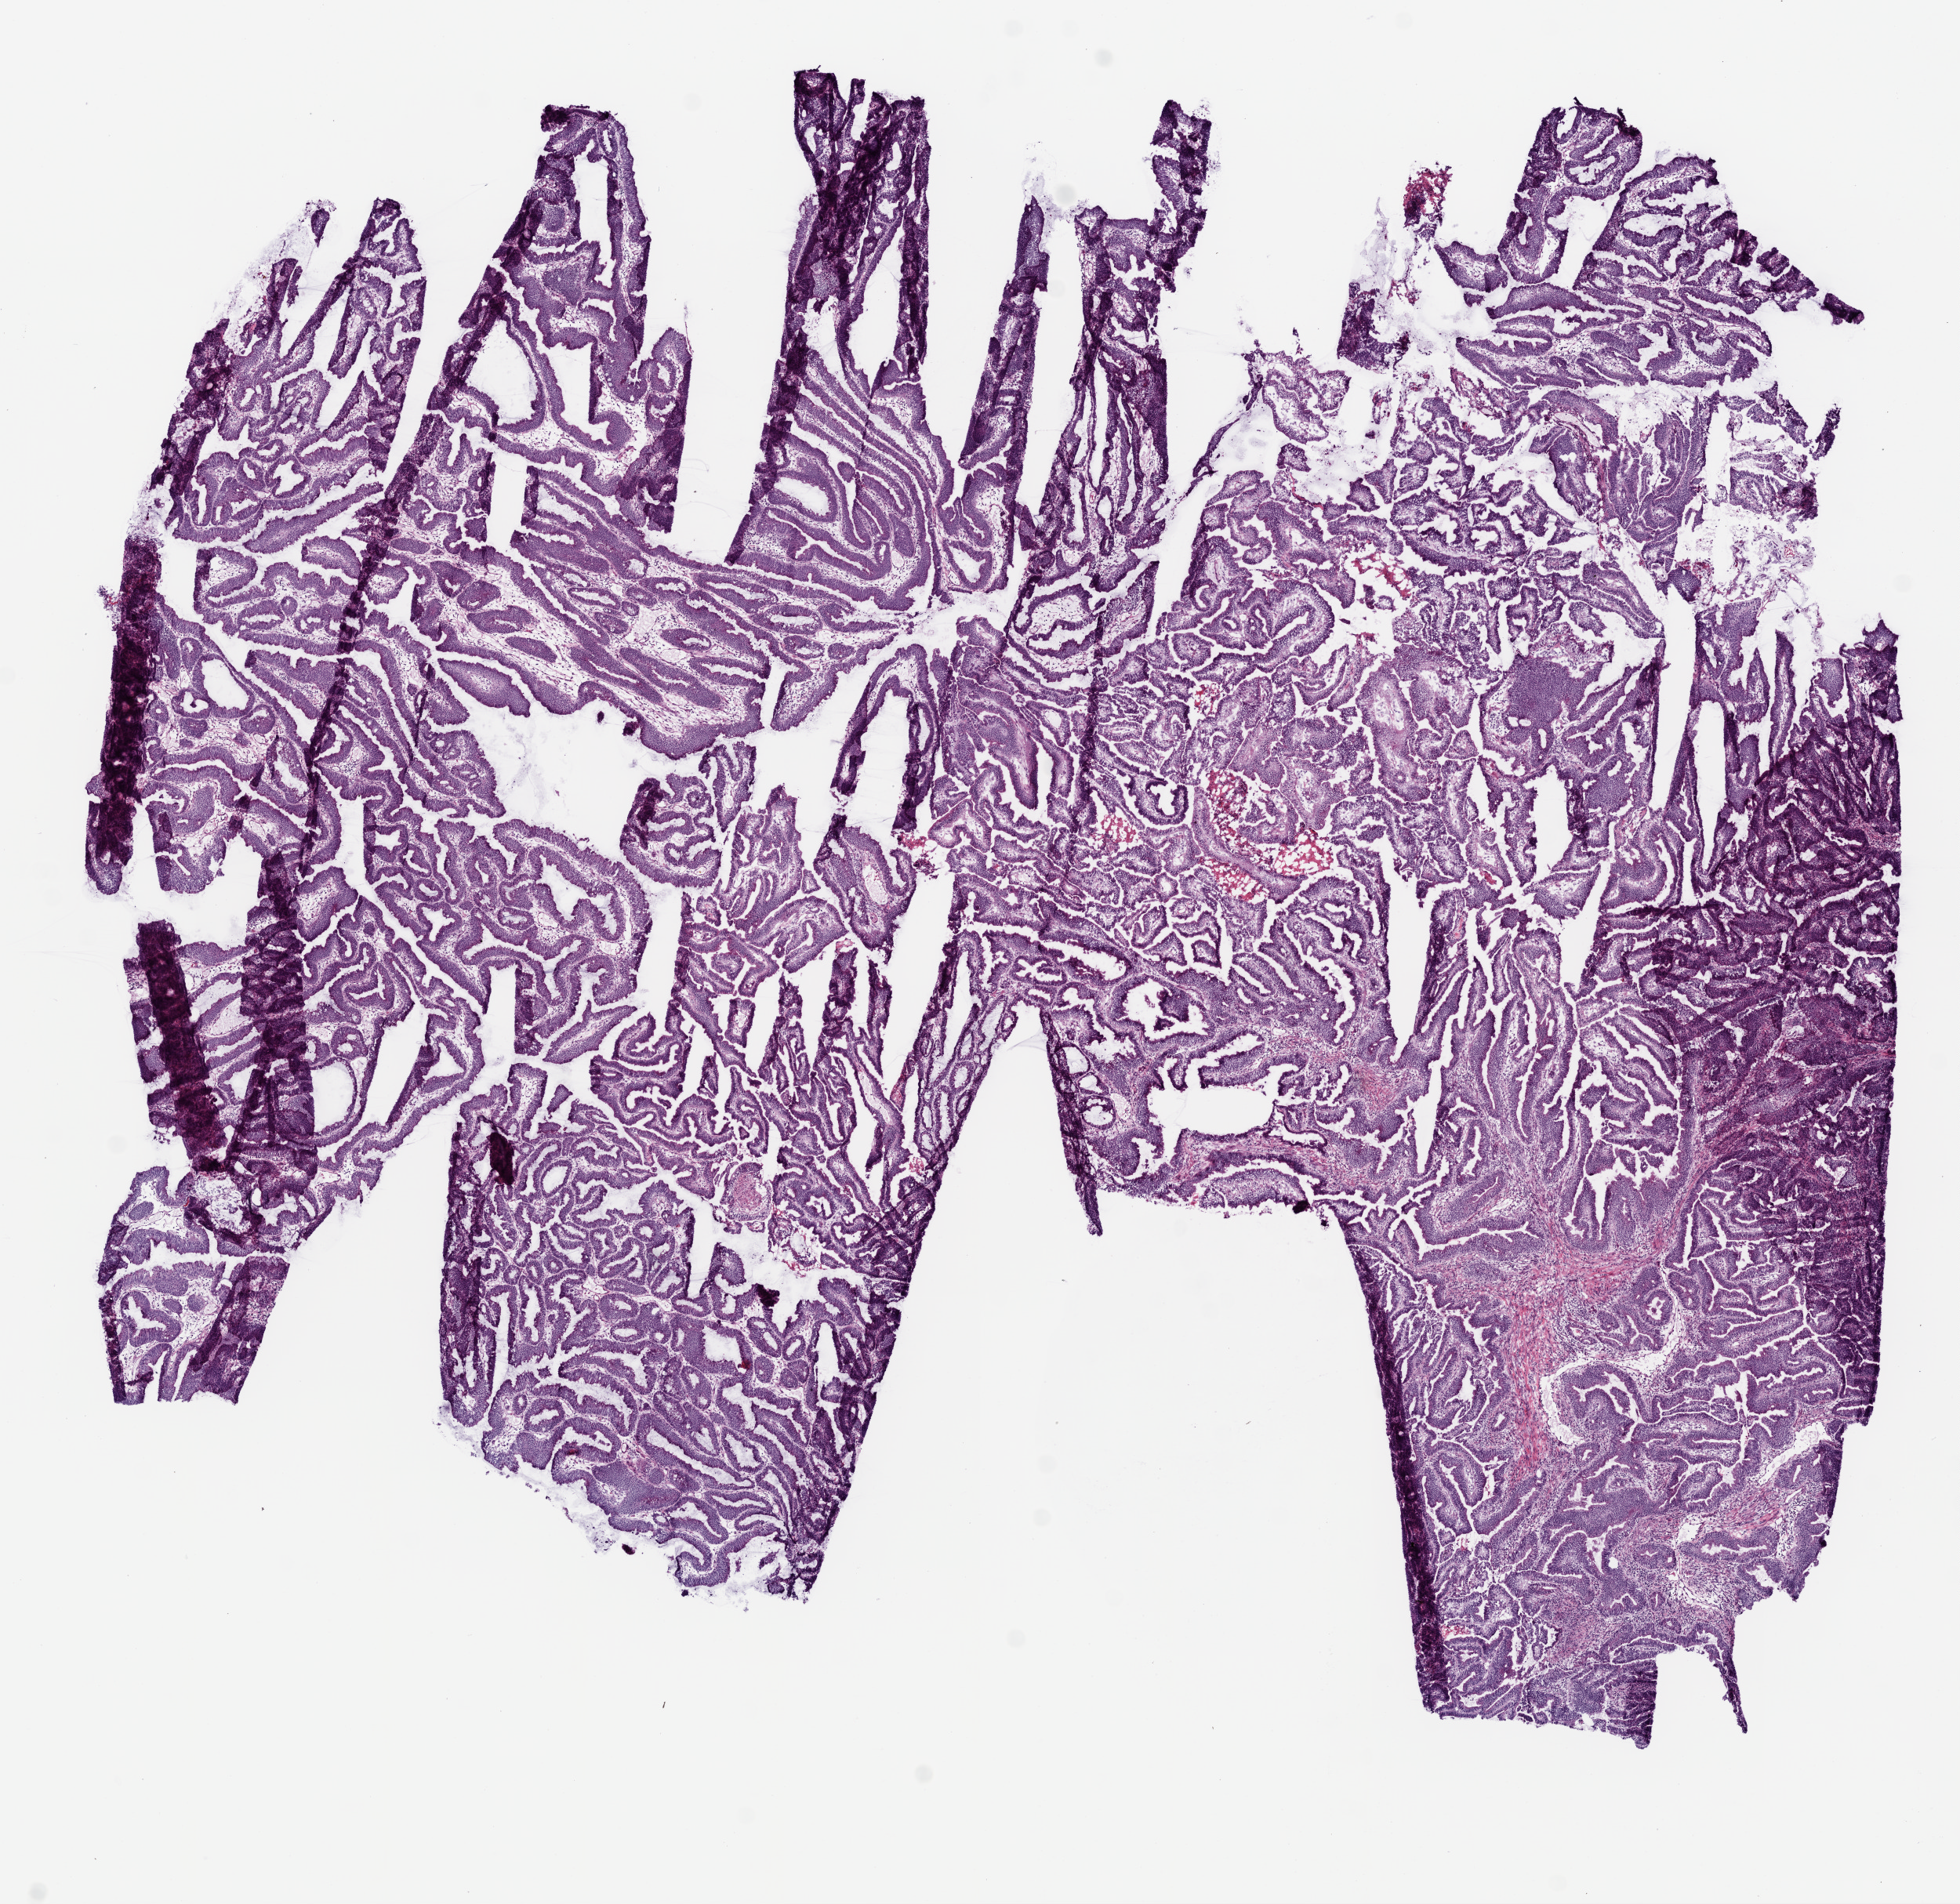
H&E-stained whole-slide image — a low-resolution overview of the entire scanned area, about 10.0 x 9.7 mm (slide scanned at 20x); frozen section from the top of the tissue portion; sample: primary tumour, stomach. Female, age 71 years at initial diagnosis. Histologic grade: G1 (well differentiated). Pathologist review of this section (percent, as recorded): tumour cells 87%, tumour nuclei 85%, normal cells 0%, stromal cells 10%, necrosis 3%.
* diagnosis: Adenocarcinoma, NOS (body of stomach)